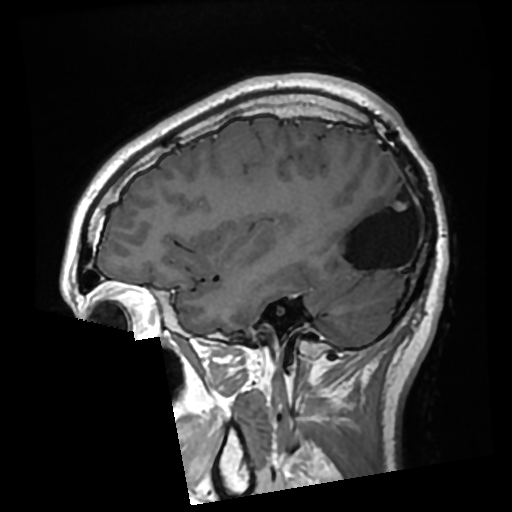
Brain MRI from a brain-tumour surgery series, one sagittal slice. Slice 89 of 276 in the series (ordered by position). T1-weighted post-contrast. 0.7 mm slice thickness. 512 × 512 image matrix. Case-level facts recorded for this patient, not image findings: histopathology: Glioma with ependymal features; WHO grade: 2.
Outlined on this slice (outlined manually by an expert reader):
- previous resection cavity: bounding box [x1, y1, x2, y2] px = [332, 182, 410, 270]
- tumour: [395, 202, 406, 211]